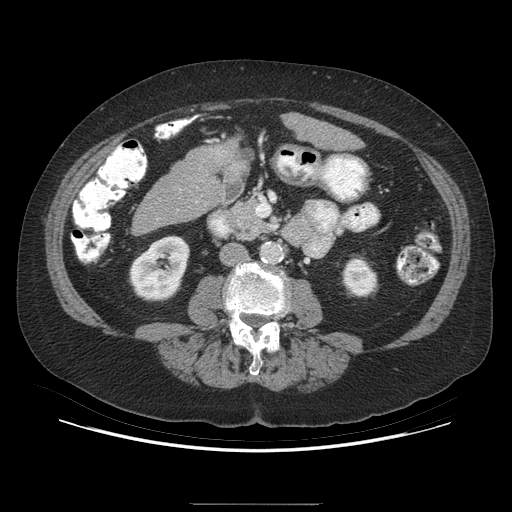
Contrast-enhanced abdominal CT (liver protocol), one axial slice. Slice 126 of 192 in the series (ordered by position). Reconstruction kernel STANDARD. 140 kVp. Soft-tissue window (W 400 / L 40 HU). 2.5 mm slice thickness. 512 × 512 image matrix, field of view 400 × 400 mm. From the clinical record (not read from this slice): diagnosis: hepatocellular carcinoma (patient treated with transarterial chemoembolisation; whether this scan precedes or follows treatment is not stated here); TNM stage (as recorded): Stage-I; Child-Pugh class: A; tumour nodularity: uninodular; tumour size: 3.2 cm.
Annotated regions visible in this slice (semi-automatically segmented with operator editing):
- liver parenchyma outside the tumour (the mass and vessels are separate outlines, so this box may not span the whole liver): bounding box (x1, y1, x2, y2) in pixels: (338, 134, 360, 148)
- mass: (228, 158, 248, 177)